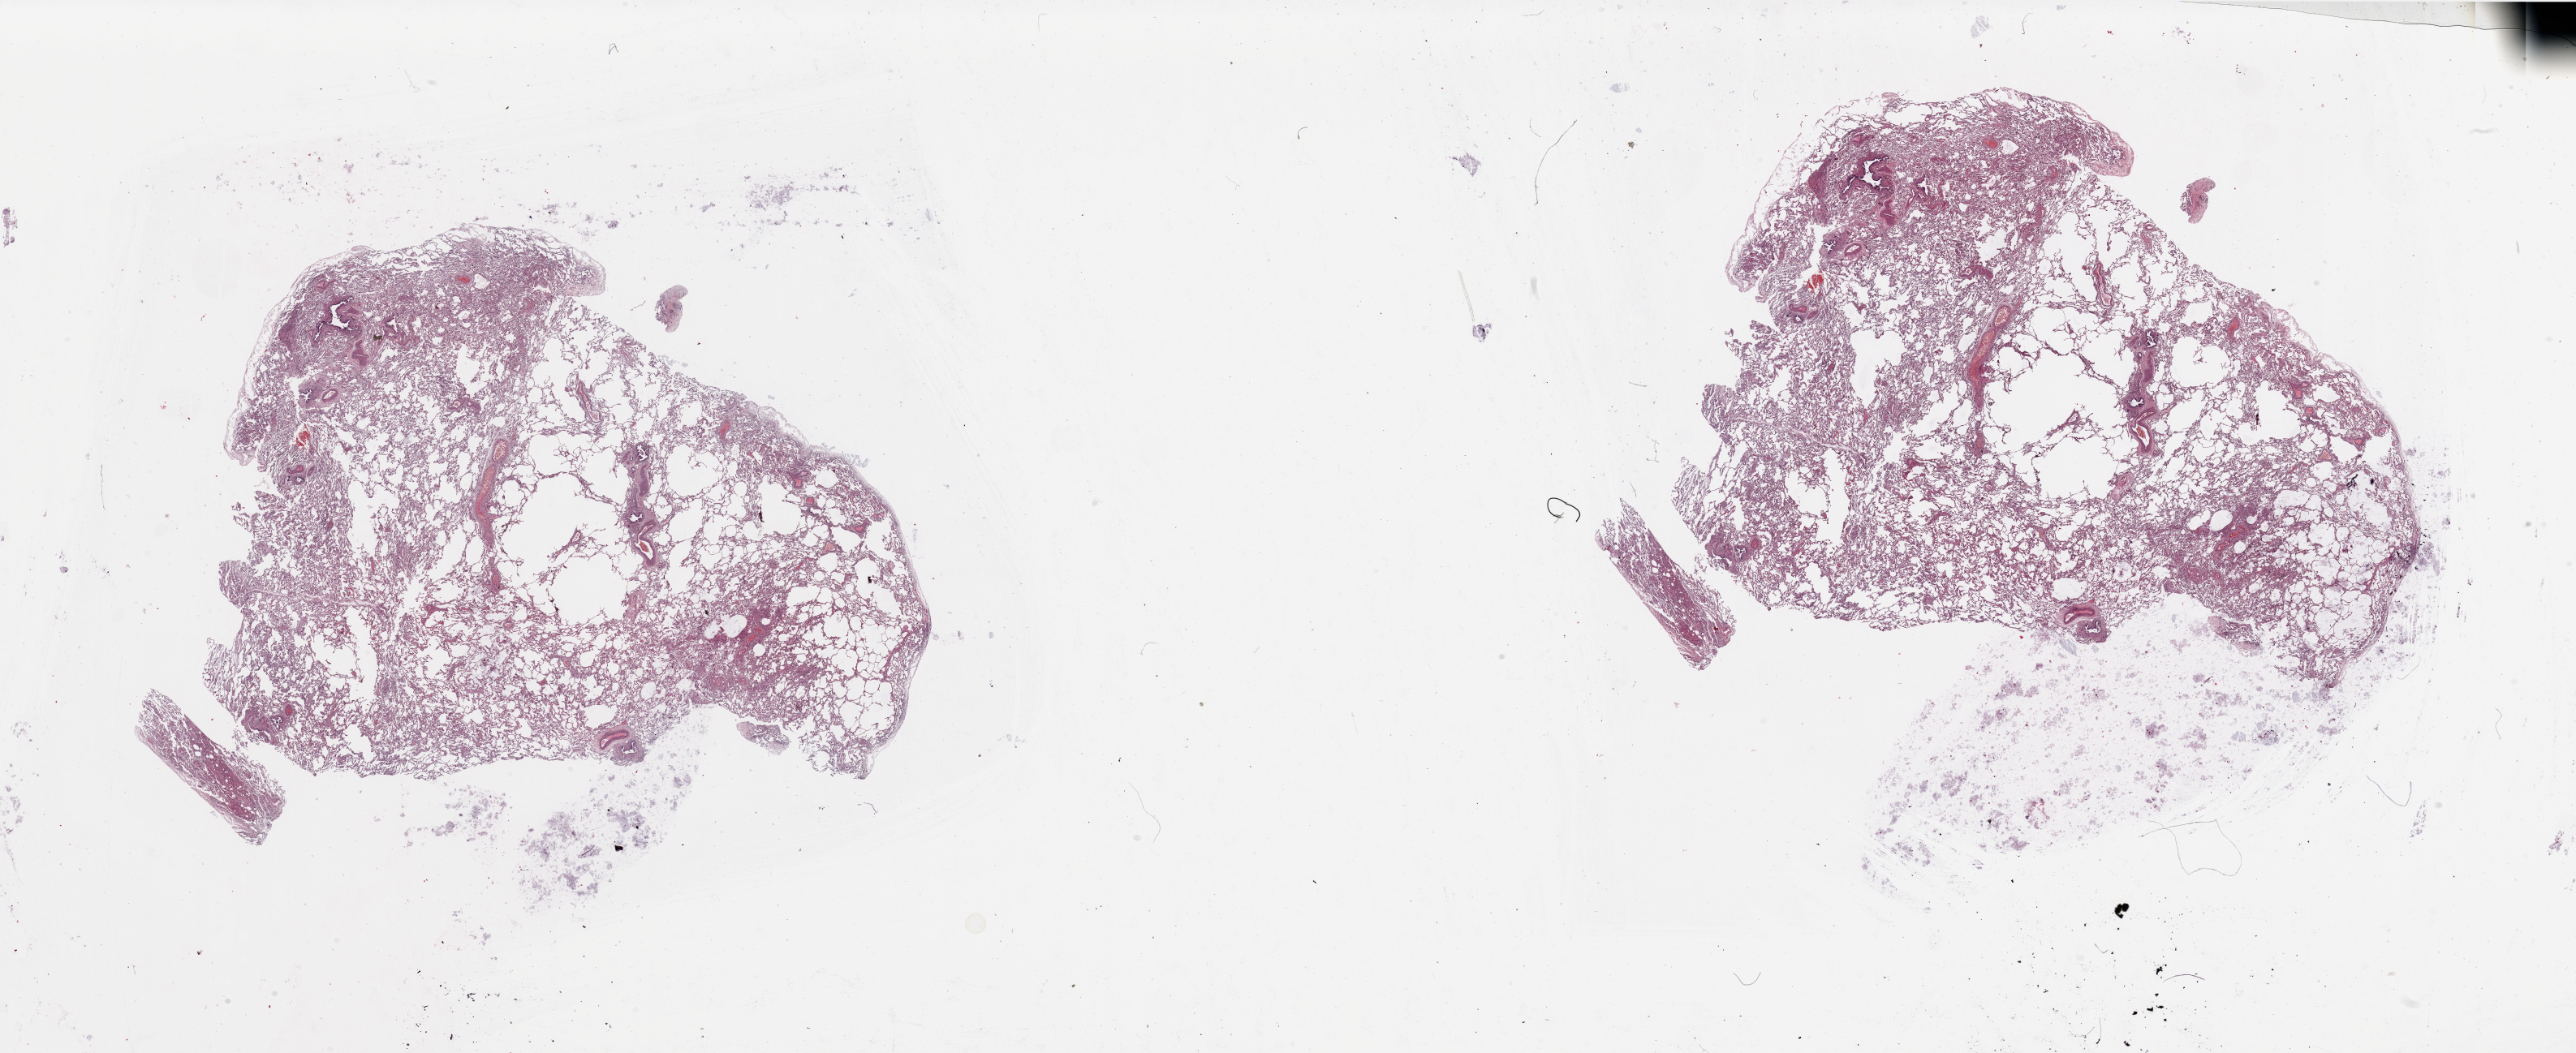
Digitized Hematoxylin and eosin (H&E) stained tissue section (whole slide) — shown as a low-resolution overview of the whole scanned area (about 50.2 x 20.5 mm, acquisition: 20x scan), normal (non-tumour) tissue sample, sampled site: lung. 61-year-old female patient.
This section: normal (non-tumour) tissue from the same patient. Patient diagnosis: Adenocarcinoma, NOS.